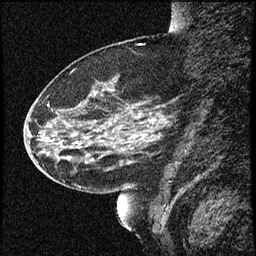
Breast MRI (dynamic contrast-enhanced), one sagittal slice; slice 23 of 60 in the series (ordered by position); dynamic contrast-enhanced study with each time point stored as its own series, time point 2 of 4 at this slice position (early post-contrast, ordered by acquisition time); 1.5 T; TE 4.2 ms, TR 16.7 ms; 2 mm slice thickness; 256 × 256 image matrix. Patient: female, 52 years. From the clinical record (not read from this slice): setting: breast cancer imaged before/during neoadjuvant chemotherapy; receptor status: HER2-positive.
Outlined on this slice (semi-automatic segmentation, software-assisted and operator-edited):
- analysis volume of interest (the breast-tissue region the enhancement analysis was run in; not a lesion): box from (x=37, y=79) to (x=165, y=181) px
- tumour enhancement mask (voxels above the 100 % enhancement threshold inside the analysis volume of interest): (x=71, y=135)–(x=136, y=163)